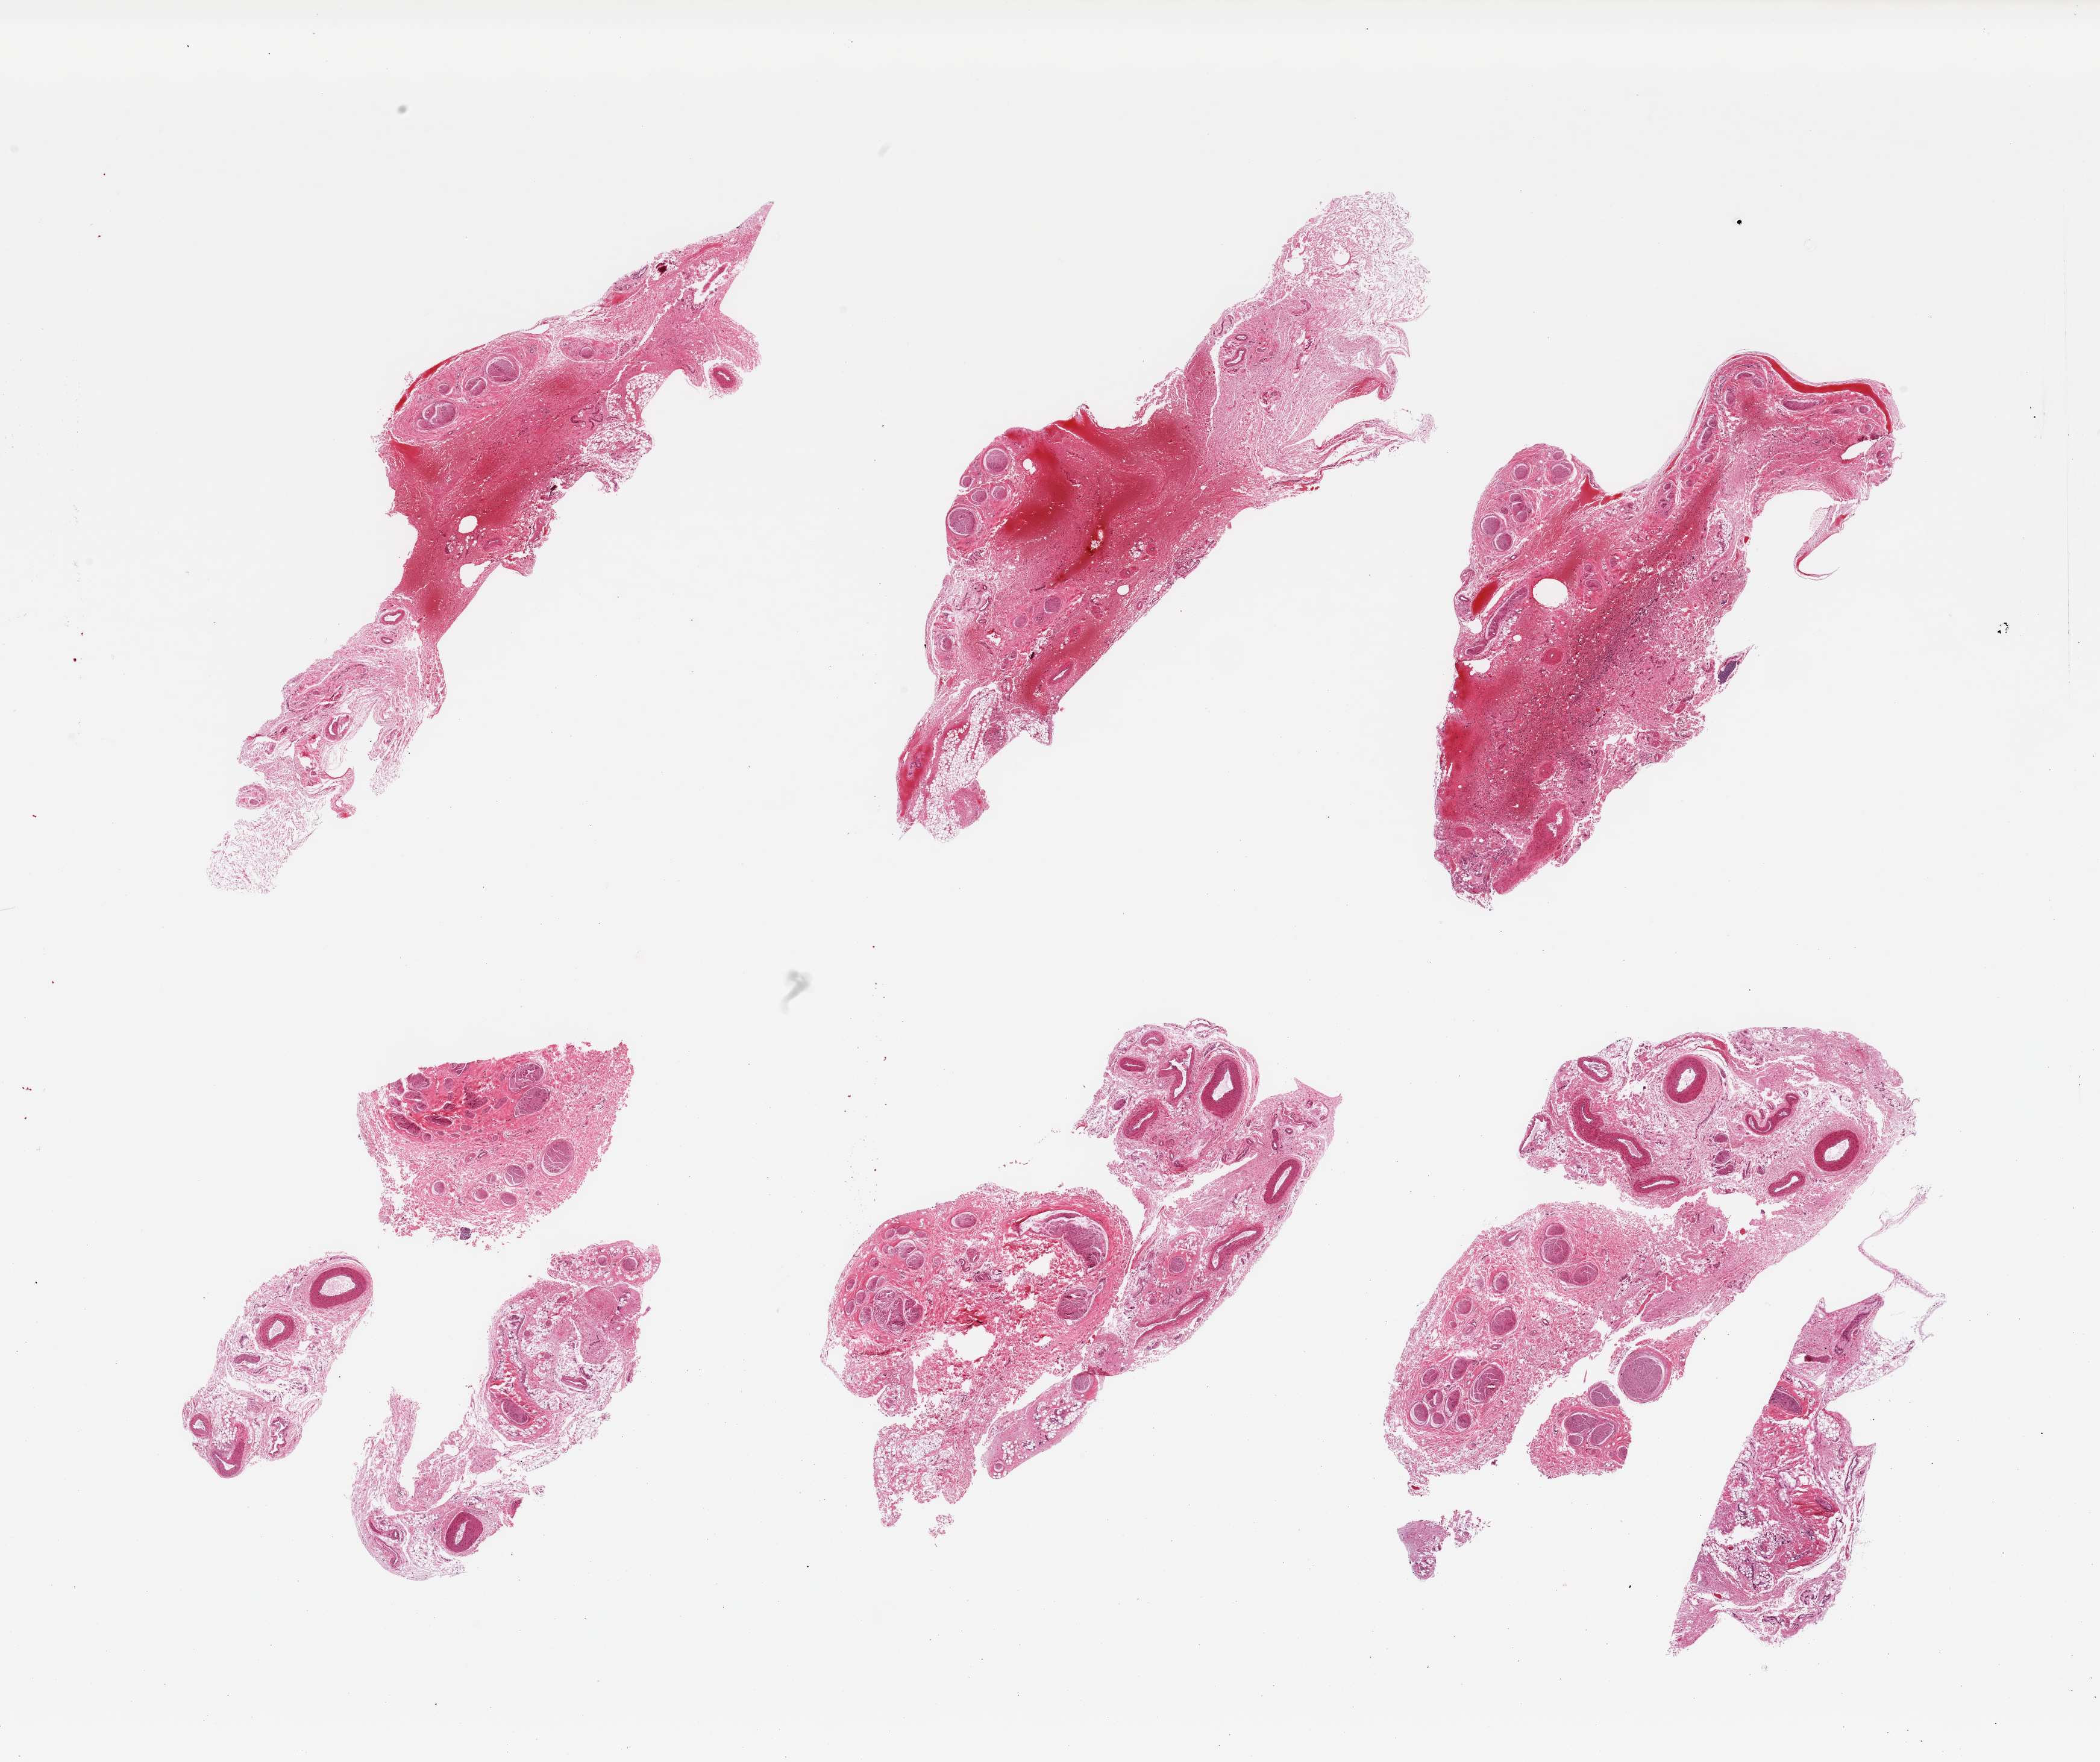
Hematoxylin and eosin (H&E) whole-slide image — whole scanned area (about 27.6 x 23.1 mm, slide scanned at 20x) shown as a low-resolution overview. PAXgene-fixed paraffin-embedded (PFPE) section. Target tissue: esophageal mucous membrane. Tissue donor sample. Male donor.
Pathologist's review note for this sample: 6 pieces;congested fibrovascular tissue, nerves and fat; target mucosa not present.